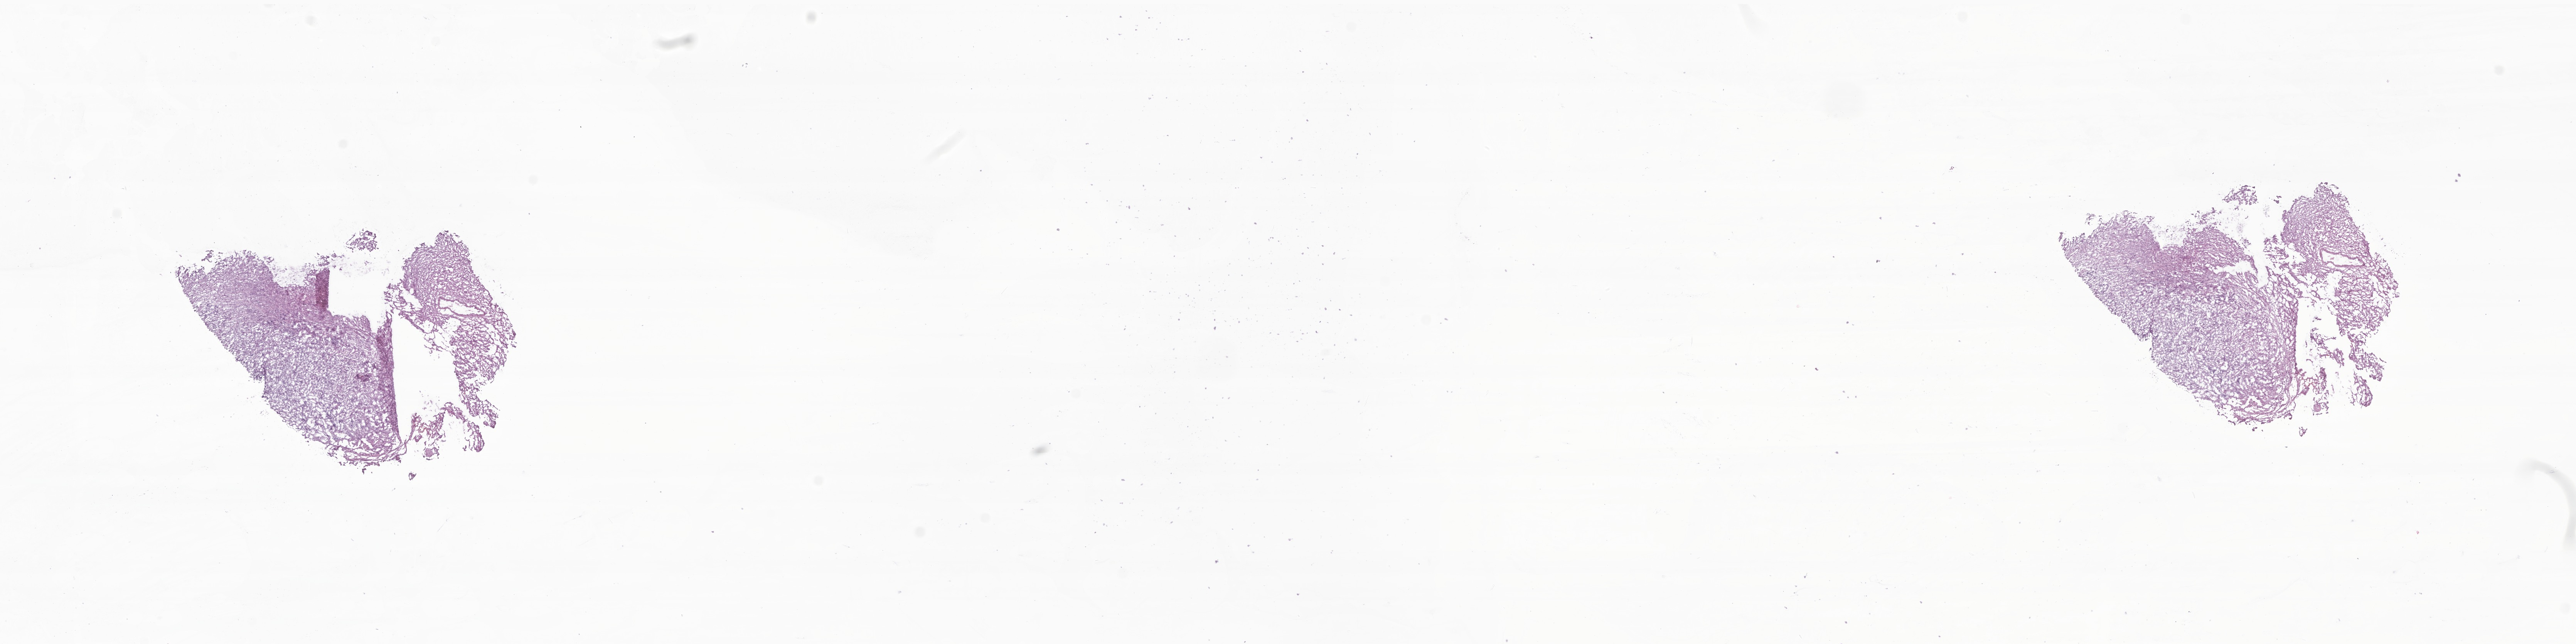
Whole-slide image, haematoxylin and eosin stain of tumor tissue from the brain, whole scanned area (about 28.2 x 7.0 mm) shown as a low-resolution overview; frozen section (OCT-embedded). Male patient, age 758 days (about 2.1 years).
Diagnosis (ICD-O-3 morphology term): Medulloblastoma, NOS.